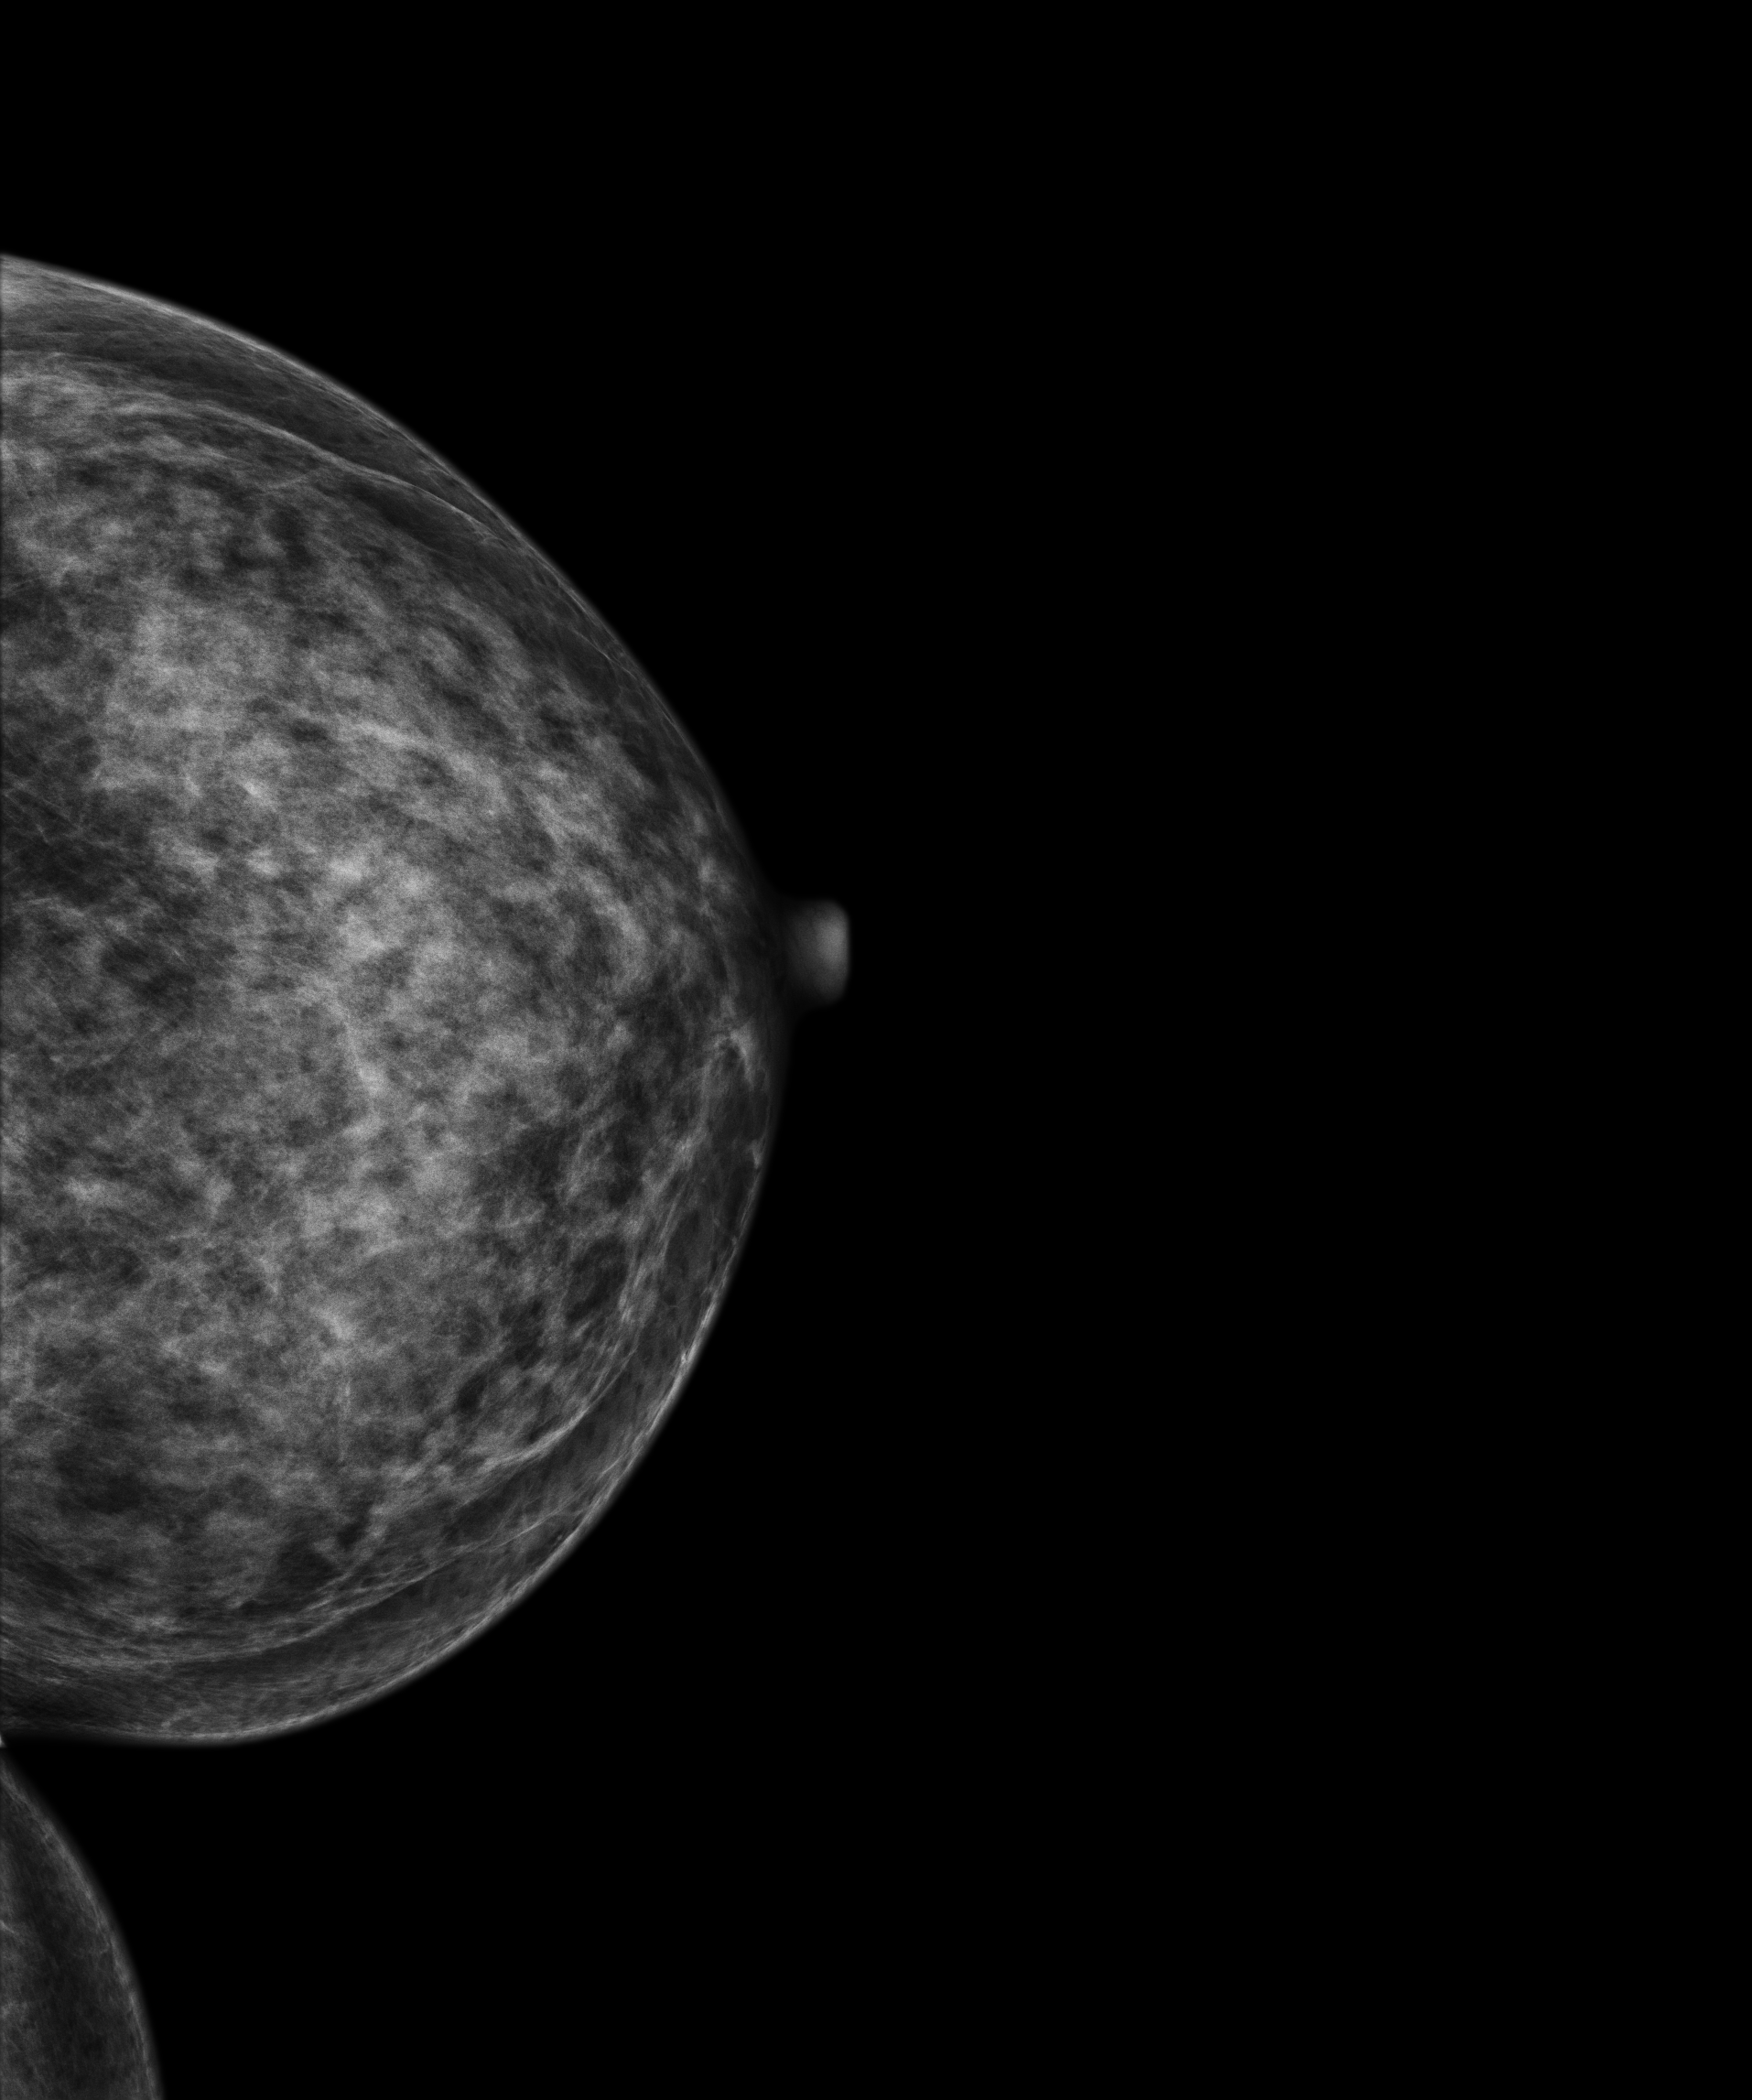
Digital mammogram (FFDM), left breast, cranio-caudal projection, screening examination, compressed breast thickness 49 mm, system: Senographe Essential ADS_56.21.3. Patient aged 60 years (female).
- BI-RADS breast density category at the screening exam (both breasts, scale 1–4): 4
- final BI-RADS category for the screening round (tomosynthesis exam, both breasts): category 1
- recall: no recall after this screen